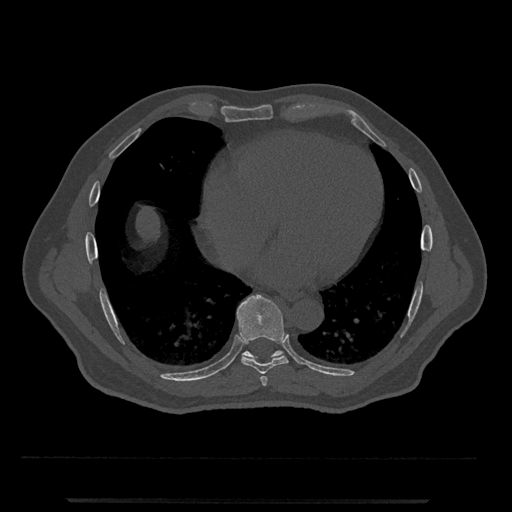
CT including the spine, one axial slice. Position 614 of 797 along the scan axis. Reconstruction kernel Br40s/3. Bone window (W 1800 / L 400 HU). 0.5 mm slice thickness. 512 × 512 image matrix. Male patient, age 63 years. From the clinical record (not read from this slice): primary cancer: prostate.
Annotated regions visible in this slice (semi-automatically segmented with operator editing):
- T7 vertebra: bounding box [x1, y1, x2, y2] px = [260, 376, 268, 386]
- T8 vertebra: [236, 295, 289, 374]
- T9 vertebra: [242, 350, 283, 361]